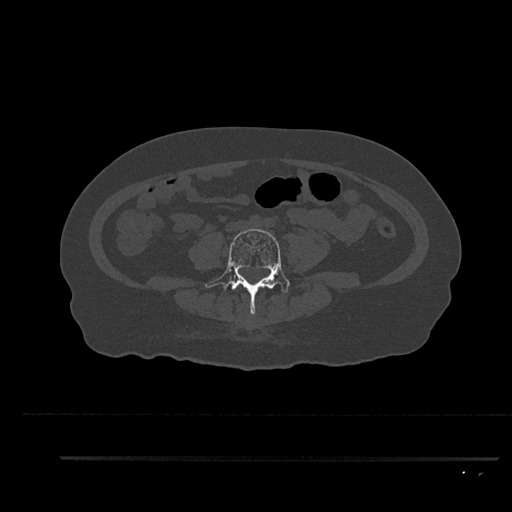
CT including the spine, one axial slice; slice 24 of 797 in the series (ordered by position); bone window (W 1800 / L 400 HU); 0.5 mm slice thickness; 512 × 512 image matrix, field of view 408 × 408 mm. Female patient, age 44 years. From the clinical record (not read from this slice): primary cancer: renal; vertebrae with lytic lesions (as recorded): L1.
Annotated regions visible in this slice (semi-automatically segmented with operator editing):
- L4 vertebra: box from (x=205, y=229) to (x=290, y=316) px